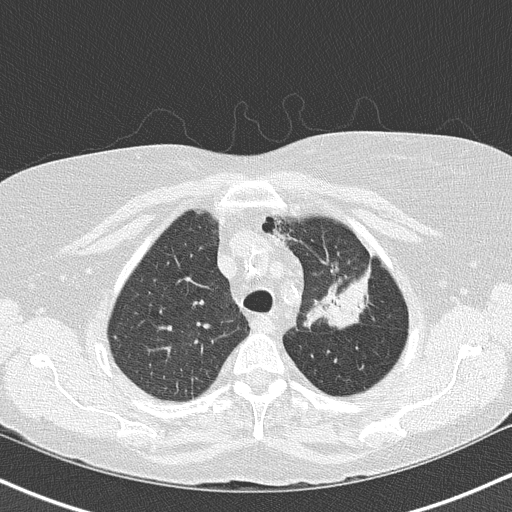
Axial slice from a low-dose chest CT screening exam; third annual screen; lung window (W 1500 / L -600 HU); 2 mm slice thickness; lung (sharp) reconstruction kernel (B50f); 120 kVp. Female, age 68 years at enrolment.
Expert-annotated lung lesion, bounding box (x1, y1, x2, y2) in pixels: (293, 226, 380, 333). Screening reader's record for this exam (one nodule recorded; not confirmed to be the boxed lesion): non-calcified nodule or mass ≥4 mm, left upper lobe, 5 × 5 mm, poorly defined margins, mixed attenuation, pre-existing on the prior screen: yes; interval growth: yes. Official screen result: positive, other.